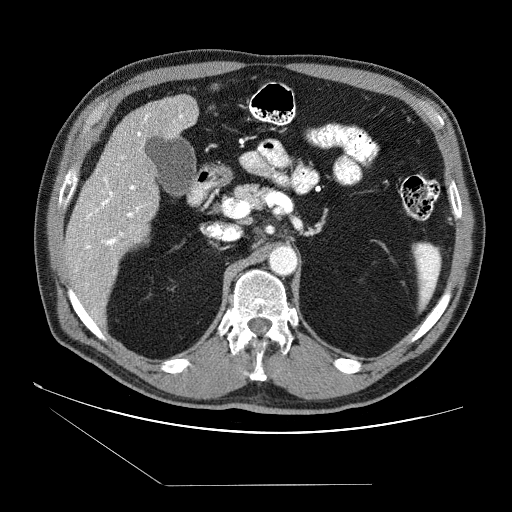
Contrast-enhanced abdominal CT (liver protocol), one axial slice. Slice 36 of 87 in the series (ordered by position). Reconstruction kernel STANDARD. Soft-tissue window (W 400 / L 40 HU). 2.5 mm slice thickness. 512 × 512 image matrix. Case-level facts recorded for this patient, not image findings: diagnosis: hepatocellular carcinoma (patient treated with transarterial chemoembolisation; whether this scan precedes or follows treatment is not stated here); TNM stage (as recorded): Stage-II; Child-Pugh class: B; tumour differentiation: no biopsy; tumour size: 2.6 cm.
Outlined on this slice (semi-automatic segmentation, software-assisted and operator-edited):
- liver parenchyma outside the tumour (the mass and vessels are separate outlines, so this box may not span the whole liver): bounding box <64,94,198,316> (left, top, right, bottom; pixels)
- liver vessels: <75,113,183,274>